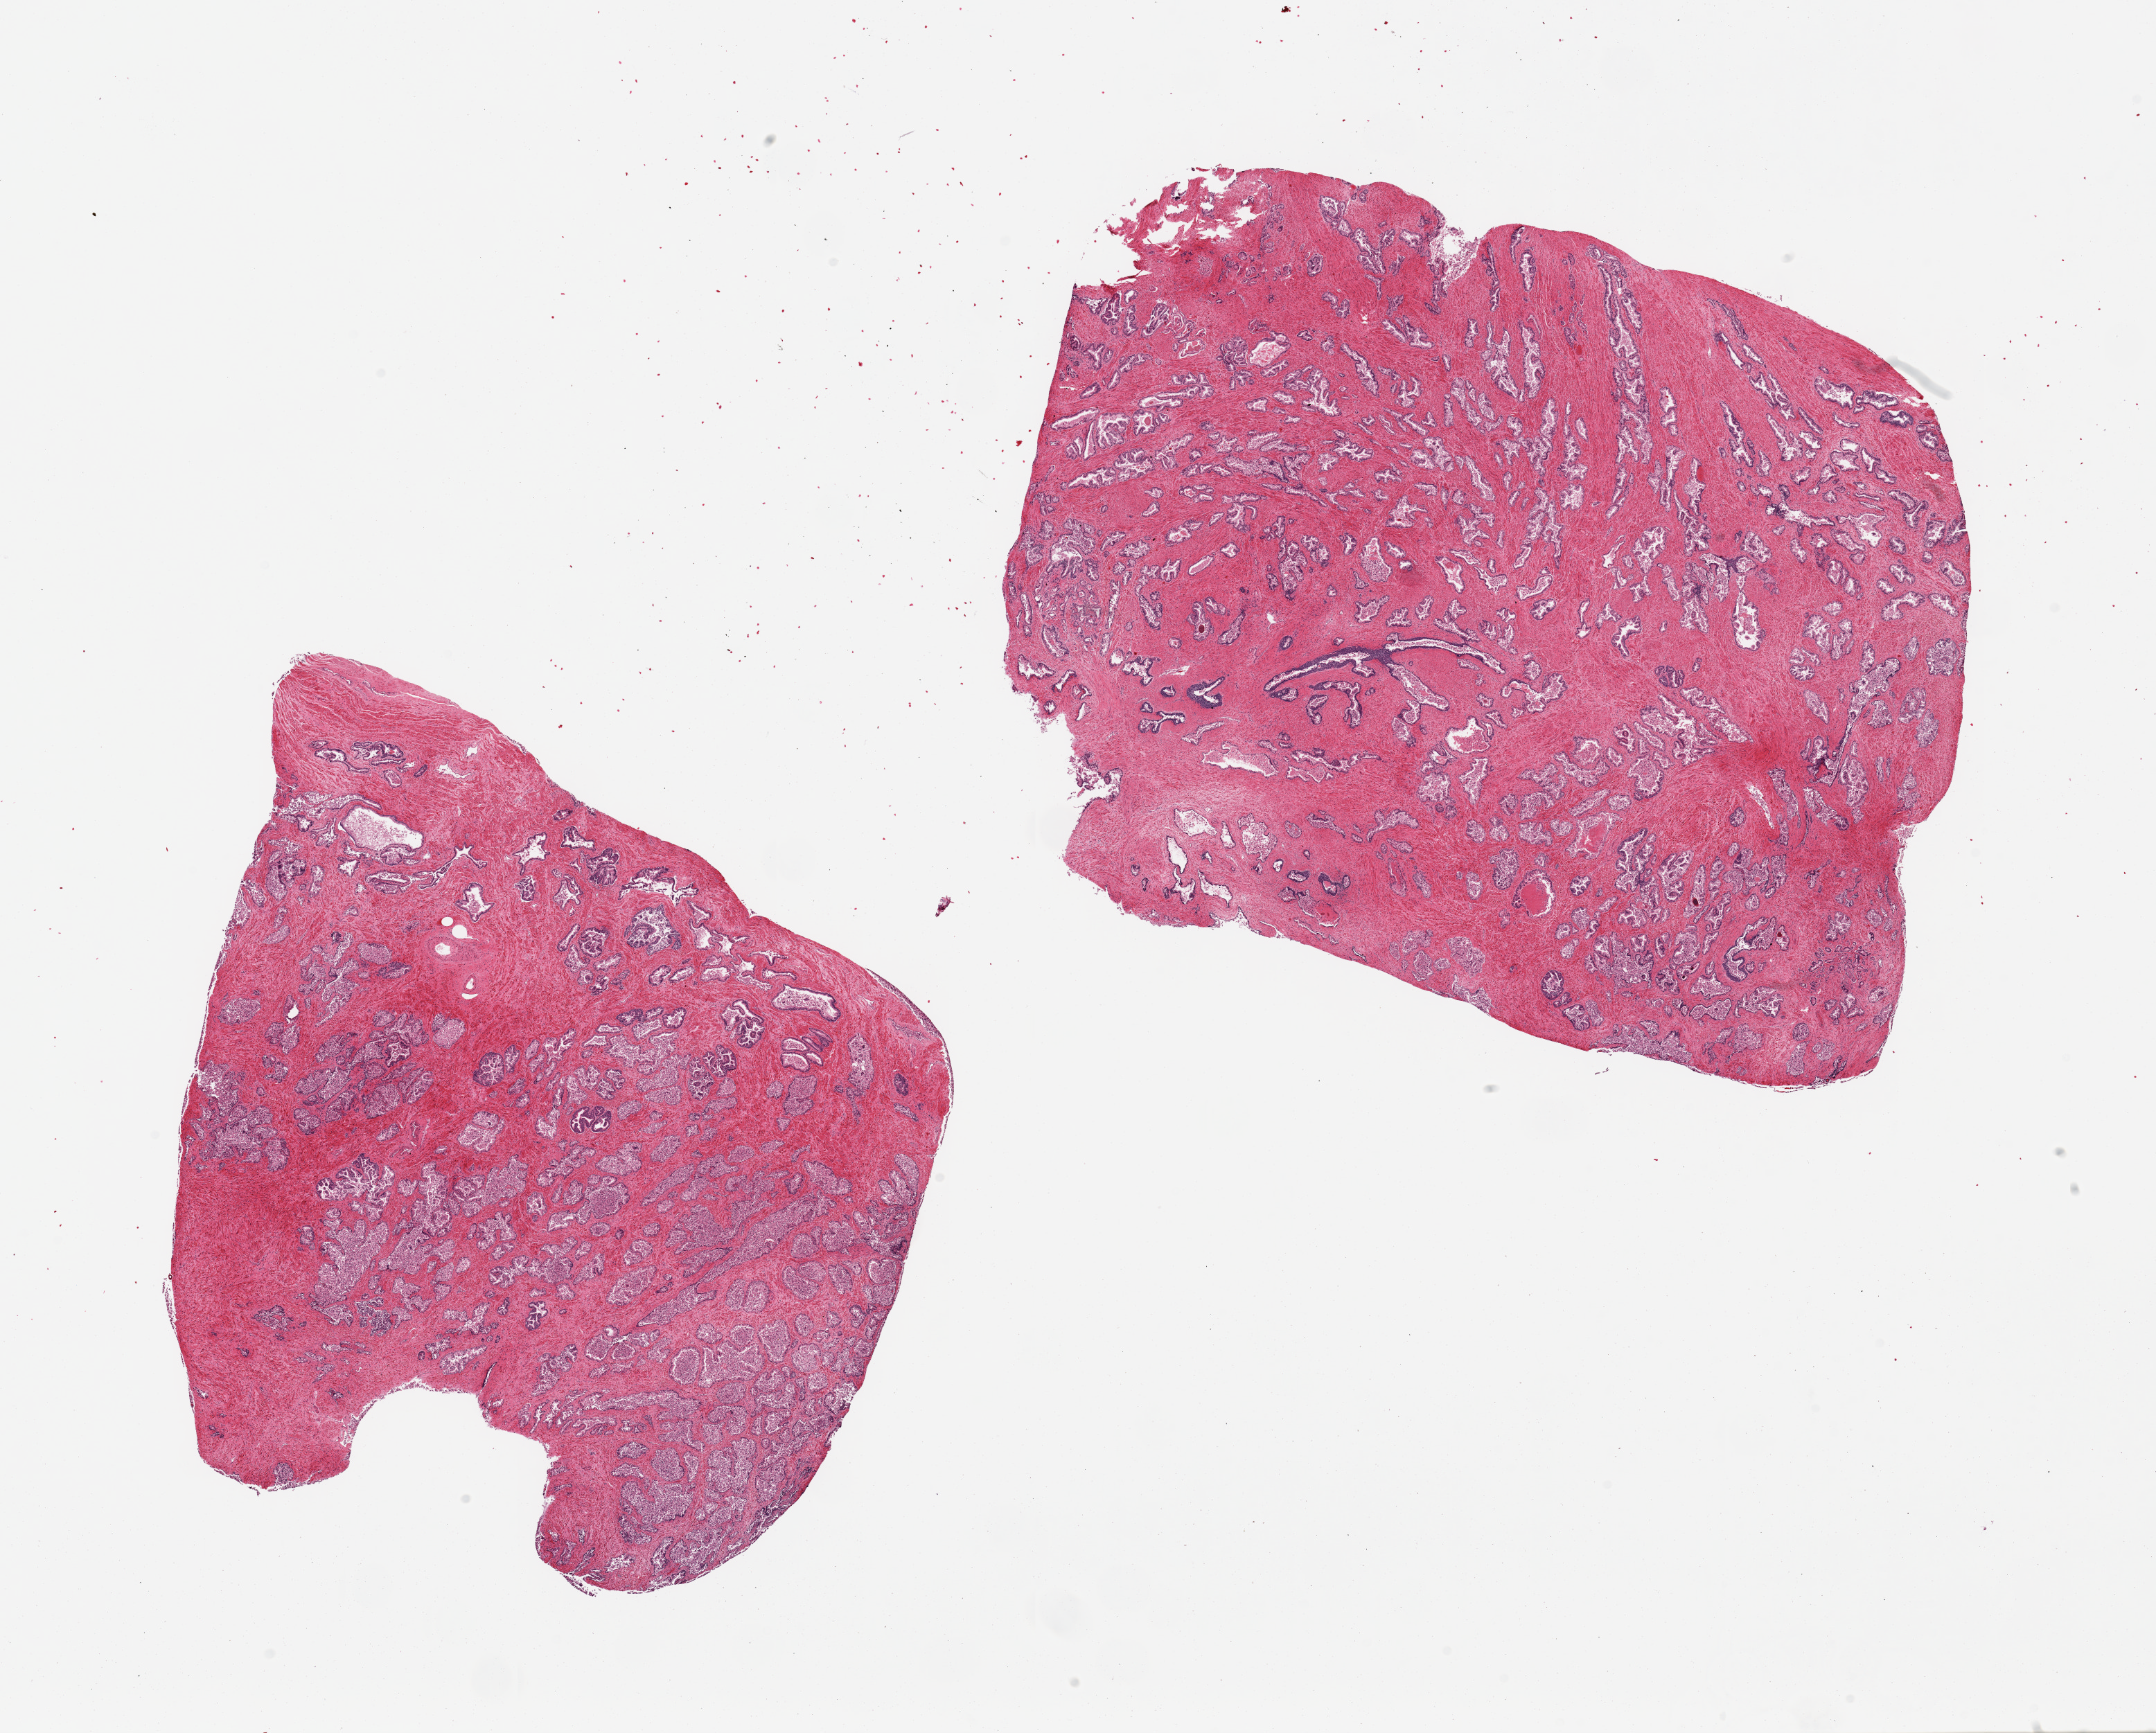
Whole-slide image, H&E stain — low-resolution overview of the scanned area, about 24.6 x 19.8 mm. PAXgene-fixed, paraffin-embedded tissue. Target tissue: prostate. Donor tissue sample. Donor: male.
Pathologist's review note for this sample: 2 pieces, hyperplastic pattern, glandular mucosa completely autolyzed.